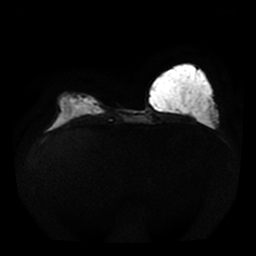
Breast MRI, one axial slice; position 13 of 41 along the scan axis; diffusion-weighted series; image 2 of 4 stored at this slice position (different b-values; order by instance number); 1.5 T; 5 mm slice thickness; 256 × 256 image matrix, field of view 330 × 330 mm. Female patient.
Outlined on this slice (manually delineated by an expert):
- tumour on diffusion-weighted imaging: bounding box [x1, y1, x2, y2] px = [70, 95, 92, 105]